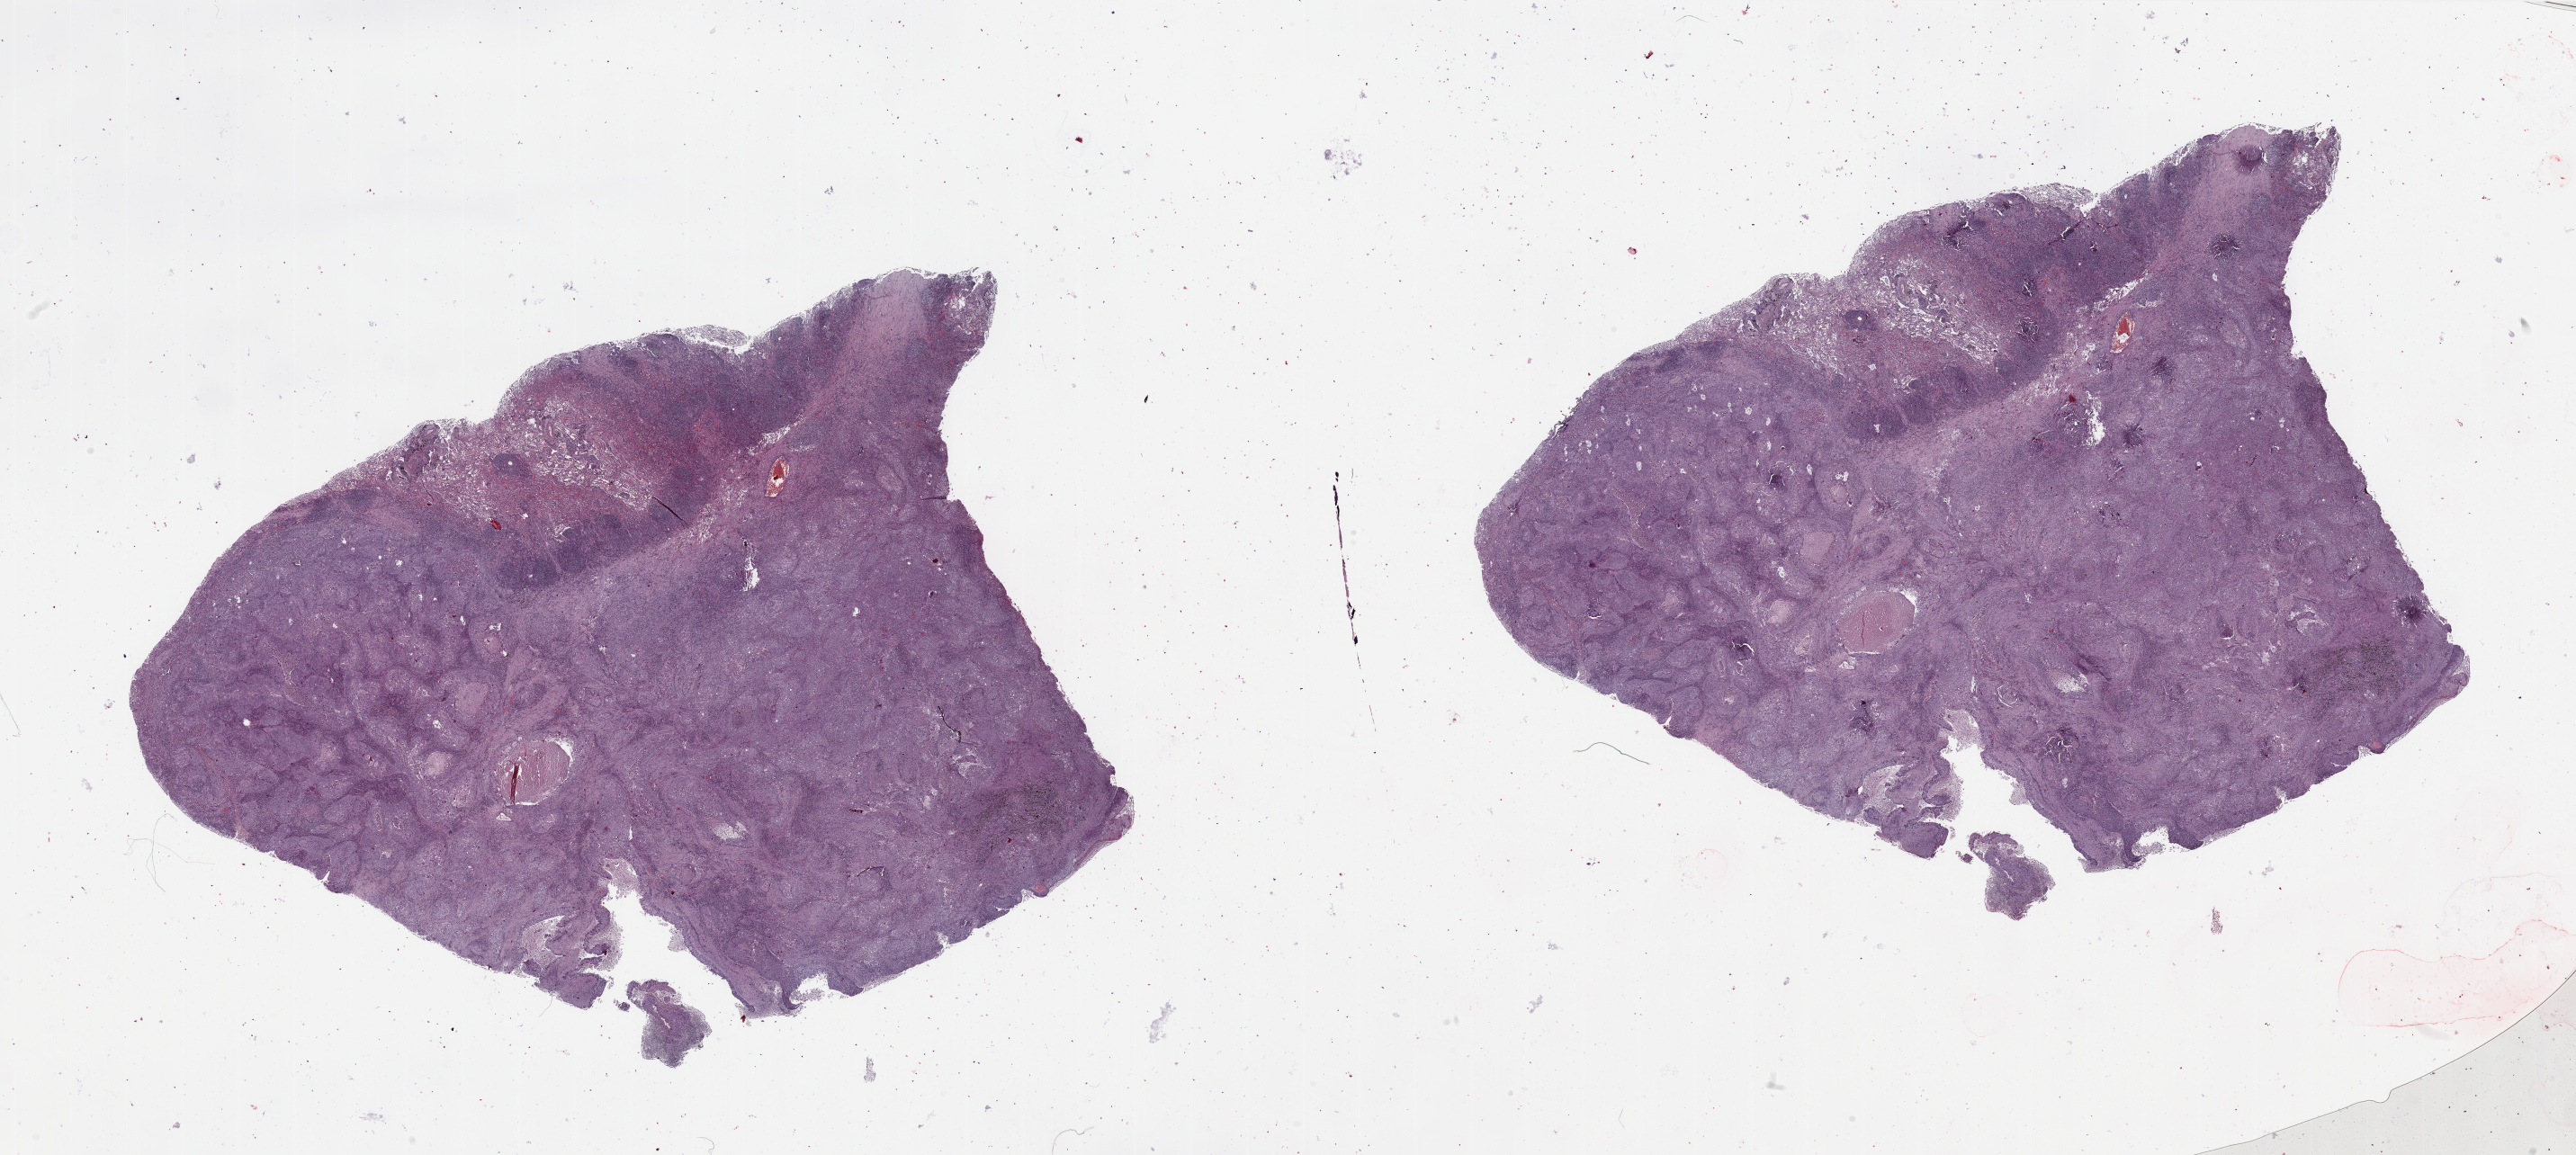
Digitized H&E tissue section (whole slide) — a low-resolution overview of the entire scanned area, about 45.3 x 20.3 mm (acquisition: 20x scan). Tumour tissue sample, sampled site: lung. Male, 70 y/o. Histologic grade: G2 (moderately differentiated). Slide review estimates, as recorded: tumour nuclei 65%, necrosis 5%.
AJCC pathologic stage: IB. Primary tumour site (as recorded): left lower lobe. Histologic diagnosis: Squamous cell carcinoma, NOS.